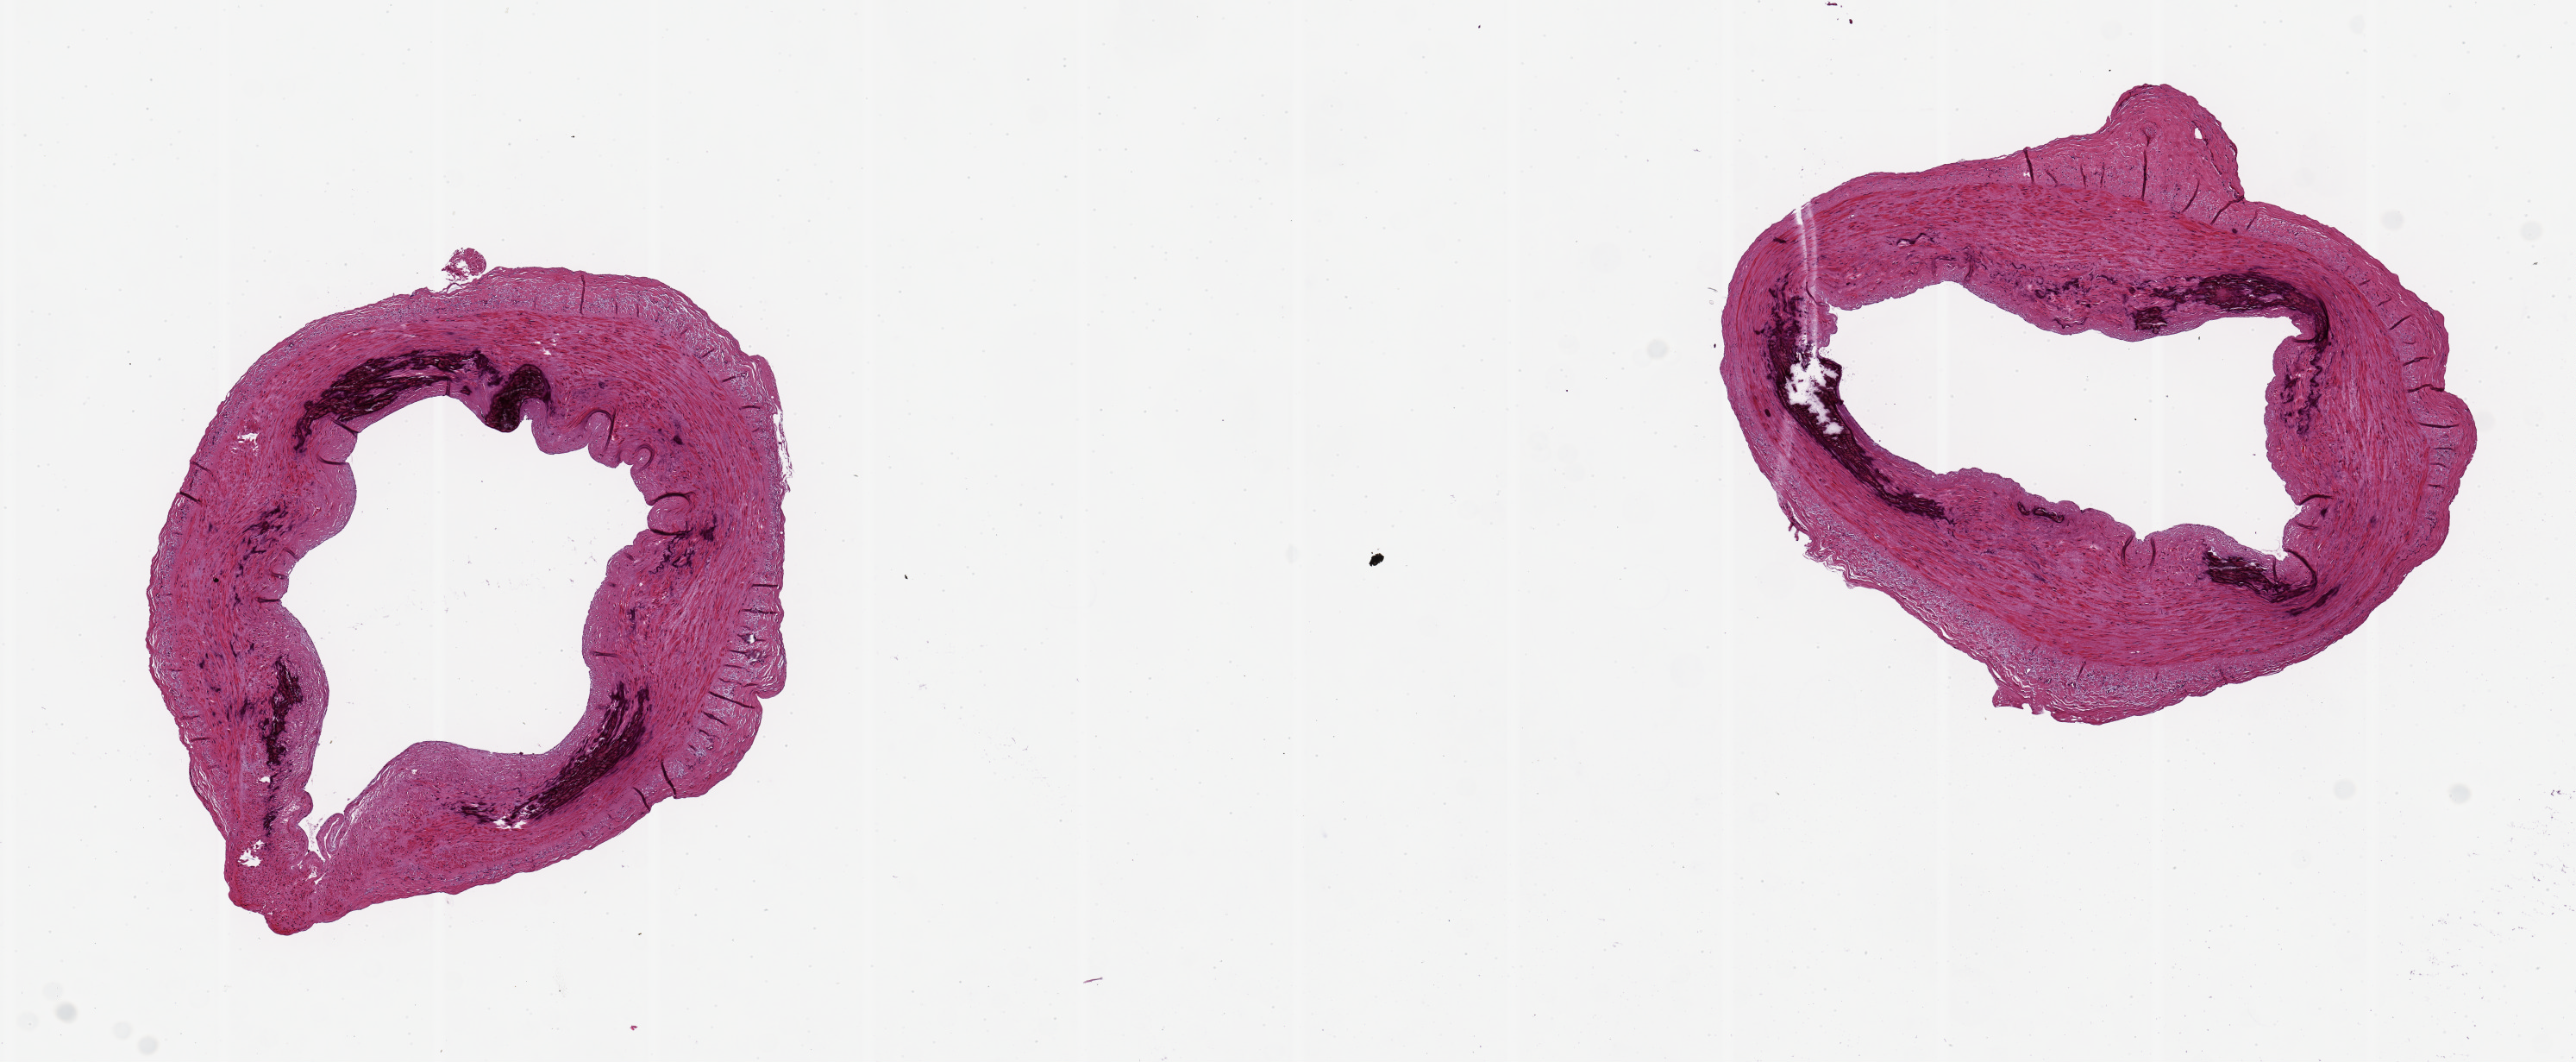
Hematoxylin and eosin (H&E) whole-slide image — low-resolution overview of the scanned area, about 11.8 x 4.9 mm. PAXgene-fixed, paraffin-embedded tissue. Section of tibial artery (target tissue). Donor tissue sample. Donor sex: male.
* reviewer comment on this tissue sample: 2 pieces ~2.6 mm; moderate Monckeberg sclerosis; clean, no adipose